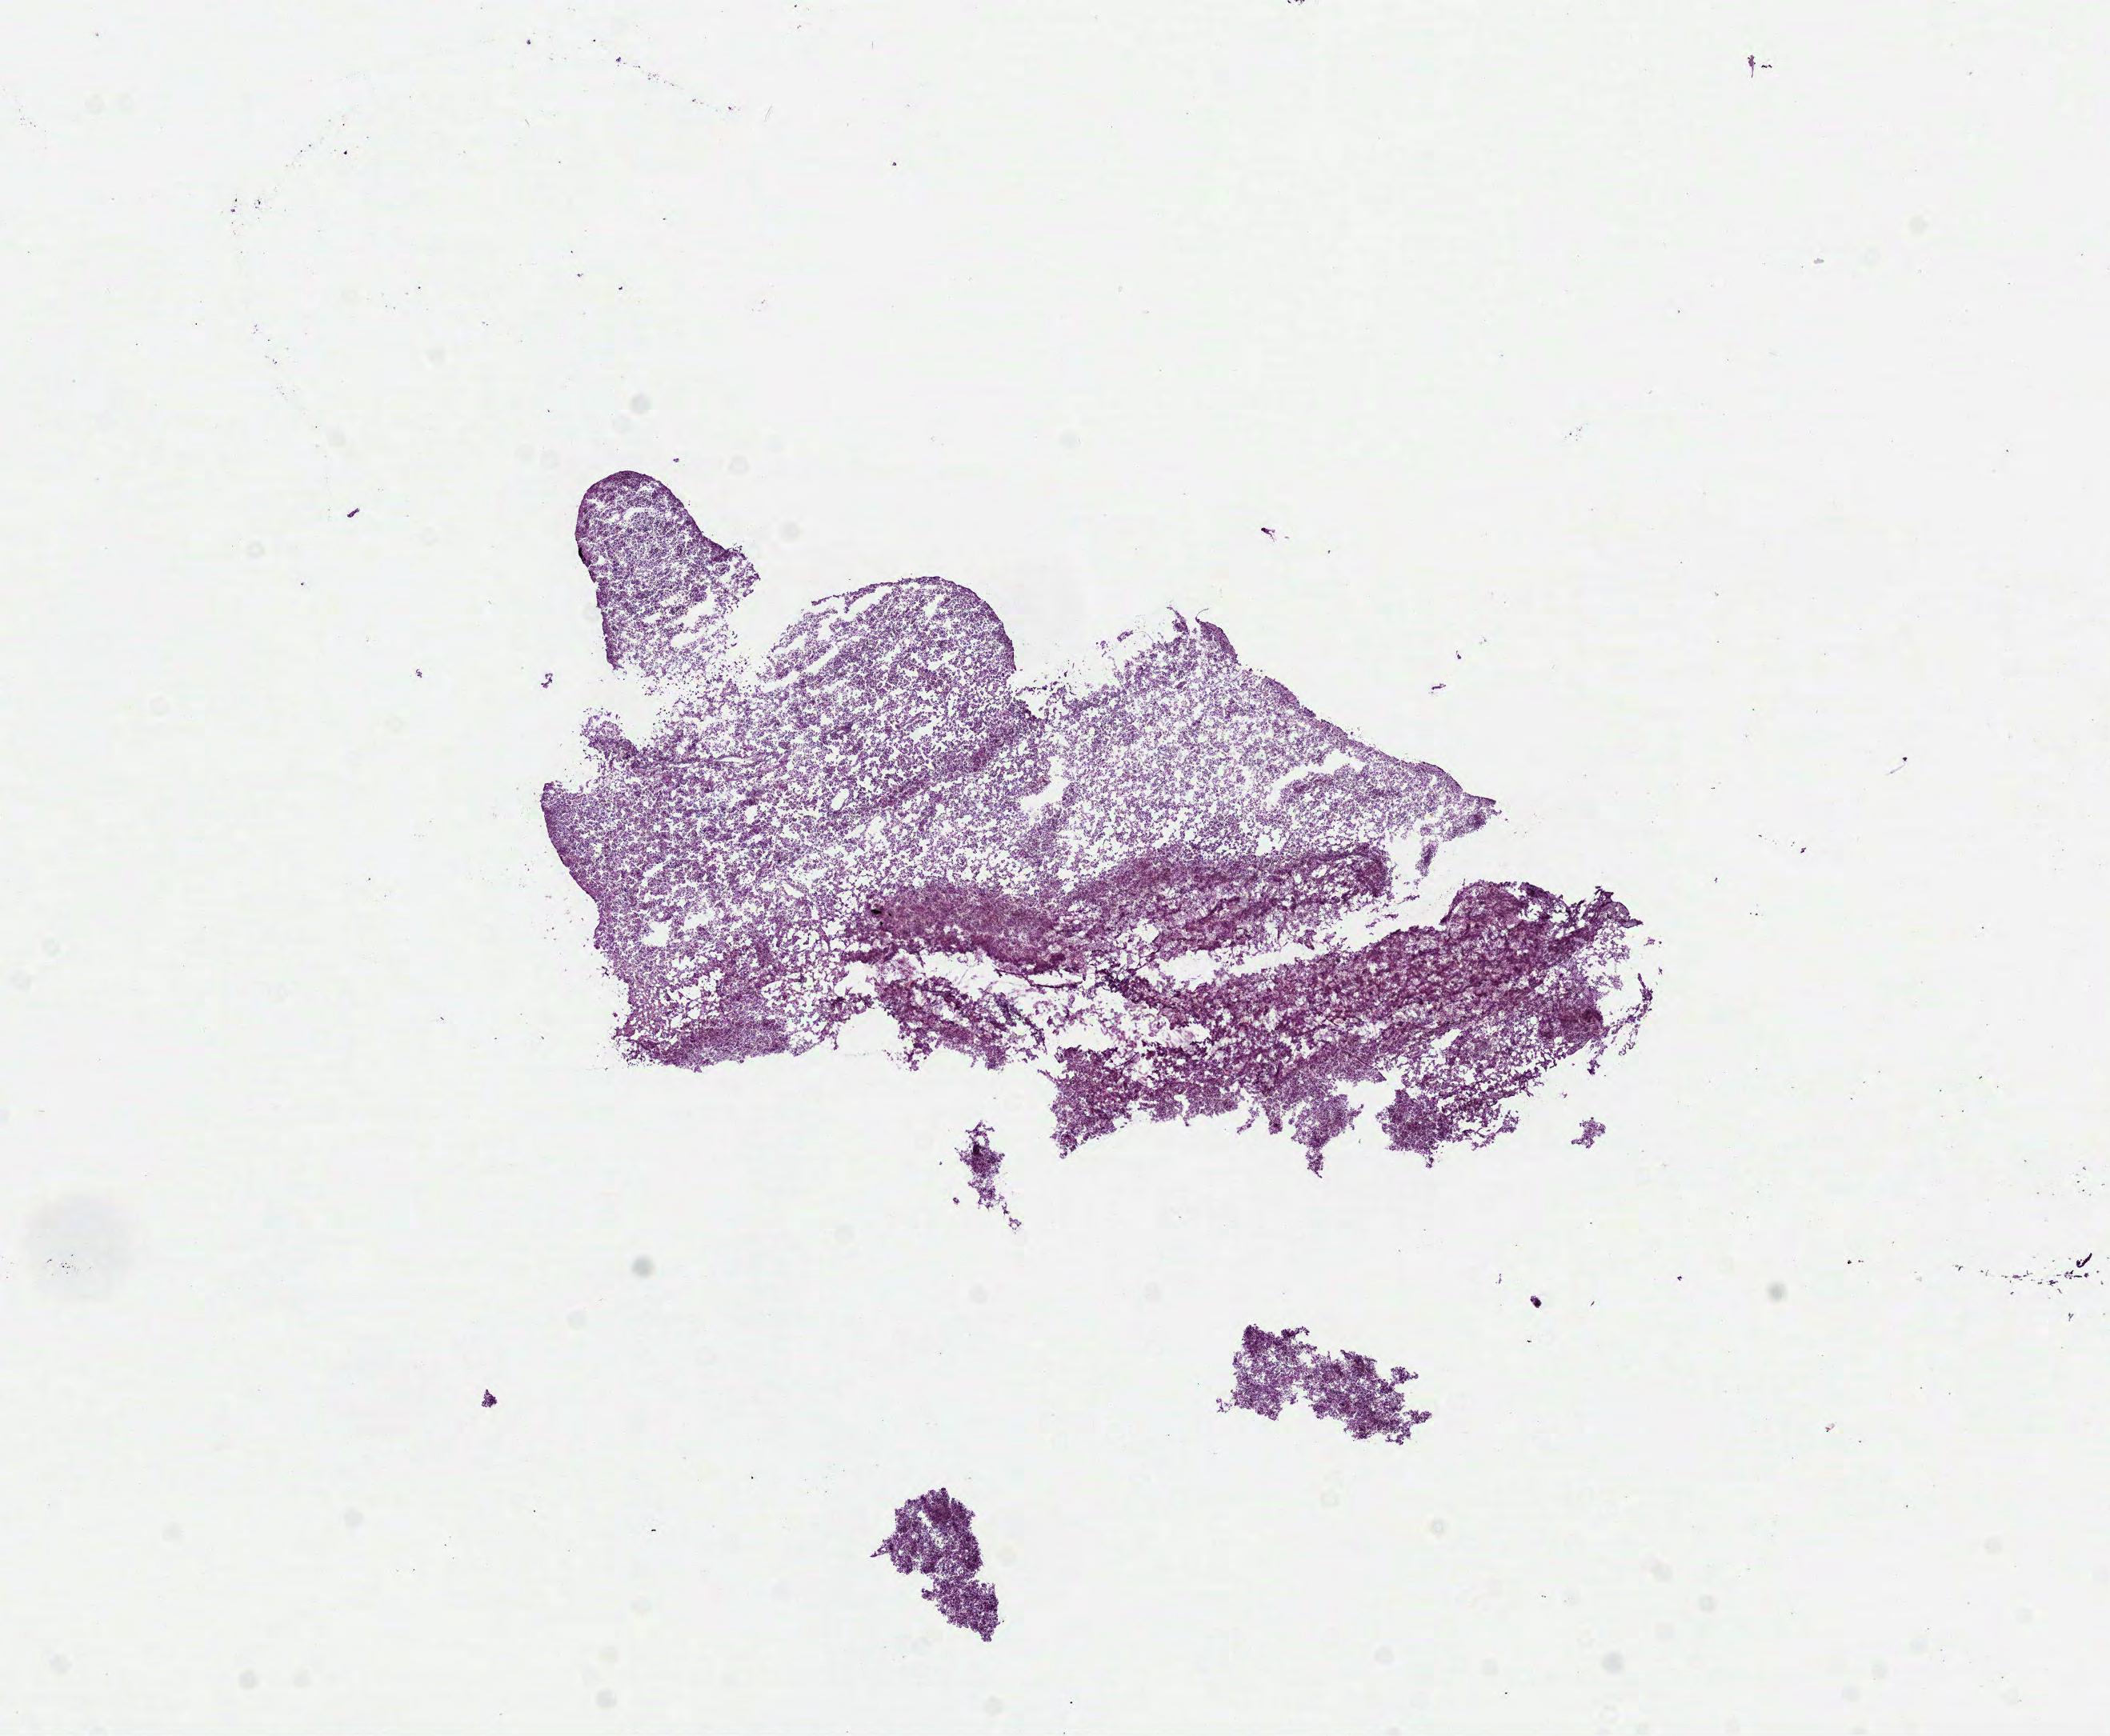
H&E-stained whole-slide image — a low-resolution overview of the entire scanned area, about 10.6 x 8.8 mm (from a 40x scan); frozen section; primary tumour sample from the lymphoid tissue. Male patient; age at initial diagnosis 67 years. Composition of this section per pathologist review: tumour cells 100%, tumour nuclei 95%, normal cells 0%, stromal cells 0%, necrosis 0%. Infiltration values recorded for this section: lymphocyte infiltration 95%, monocyte infiltration 0%, neutrophil infiltration 0%.
Histologic diagnosis: Diffuse large B-cell lymphoma, NOS.